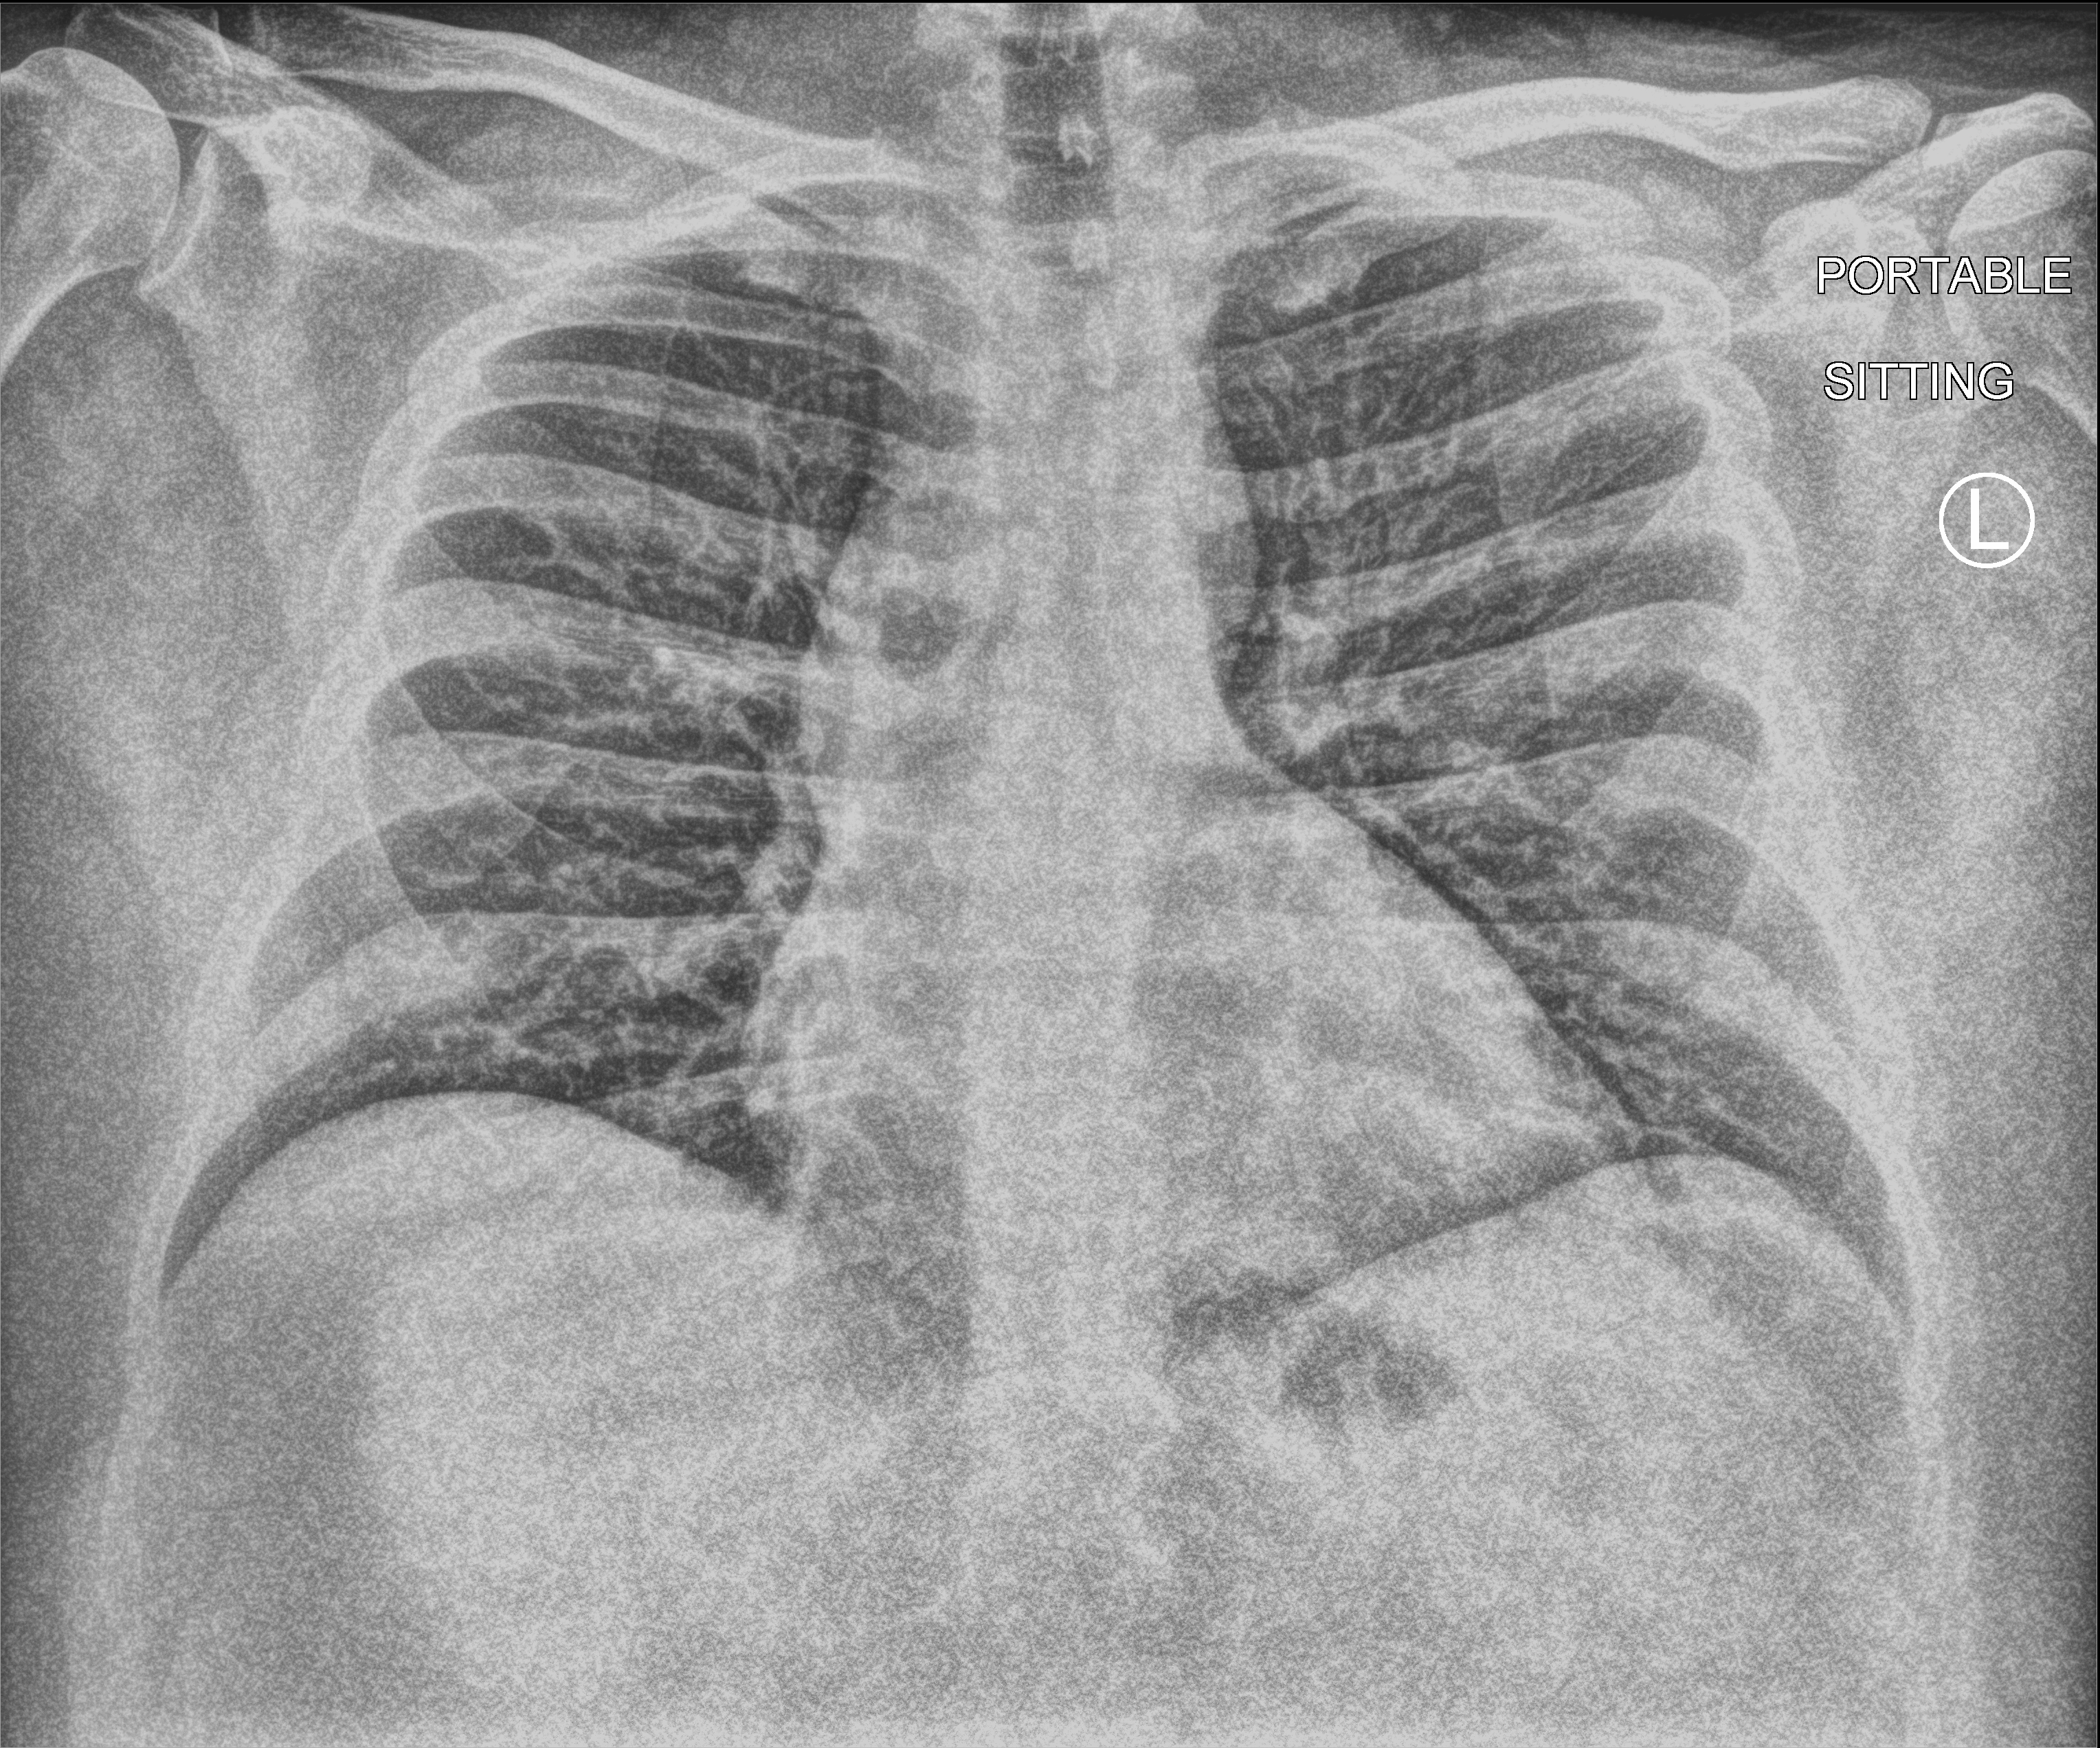
Chest X-ray (portable), anteroposterior (AP) projection. Male patient hospitalised with COVID-19, age 18–59 years.
From the hospital-stay record, not from the radiograph (when in the stay this image was taken is not recorded): mechanically ventilated during this hospital stay: no.